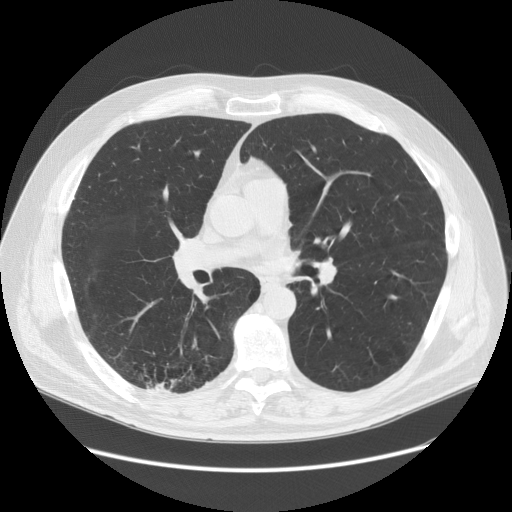
Low-dose screening chest CT, axial slice, first (baseline) screen, lung window (W 1500 / L -600 HU), 2.5 mm slice thickness. Male, age 68 years at enrolment. Former smoker at enrolment.
• Expert-annotated lung lesion, bounding box <129,343,226,416> (left, top, right, bottom; pixels).
• Reader record for this screening exam (exam-level; its link to the box is not recorded): non-calcified nodule or mass ≥4 mm, right lower lobe, 37 × 20 mm, spiculated (stellate) margins, soft tissue attenuation.
• Lung cancer was diagnosed 24 days after this screen: adenosquamous carcinoma, right lower lobe, poorly differentiated (G3), stage IIIA (AJCC 6th edition), 30 mm at pathology.